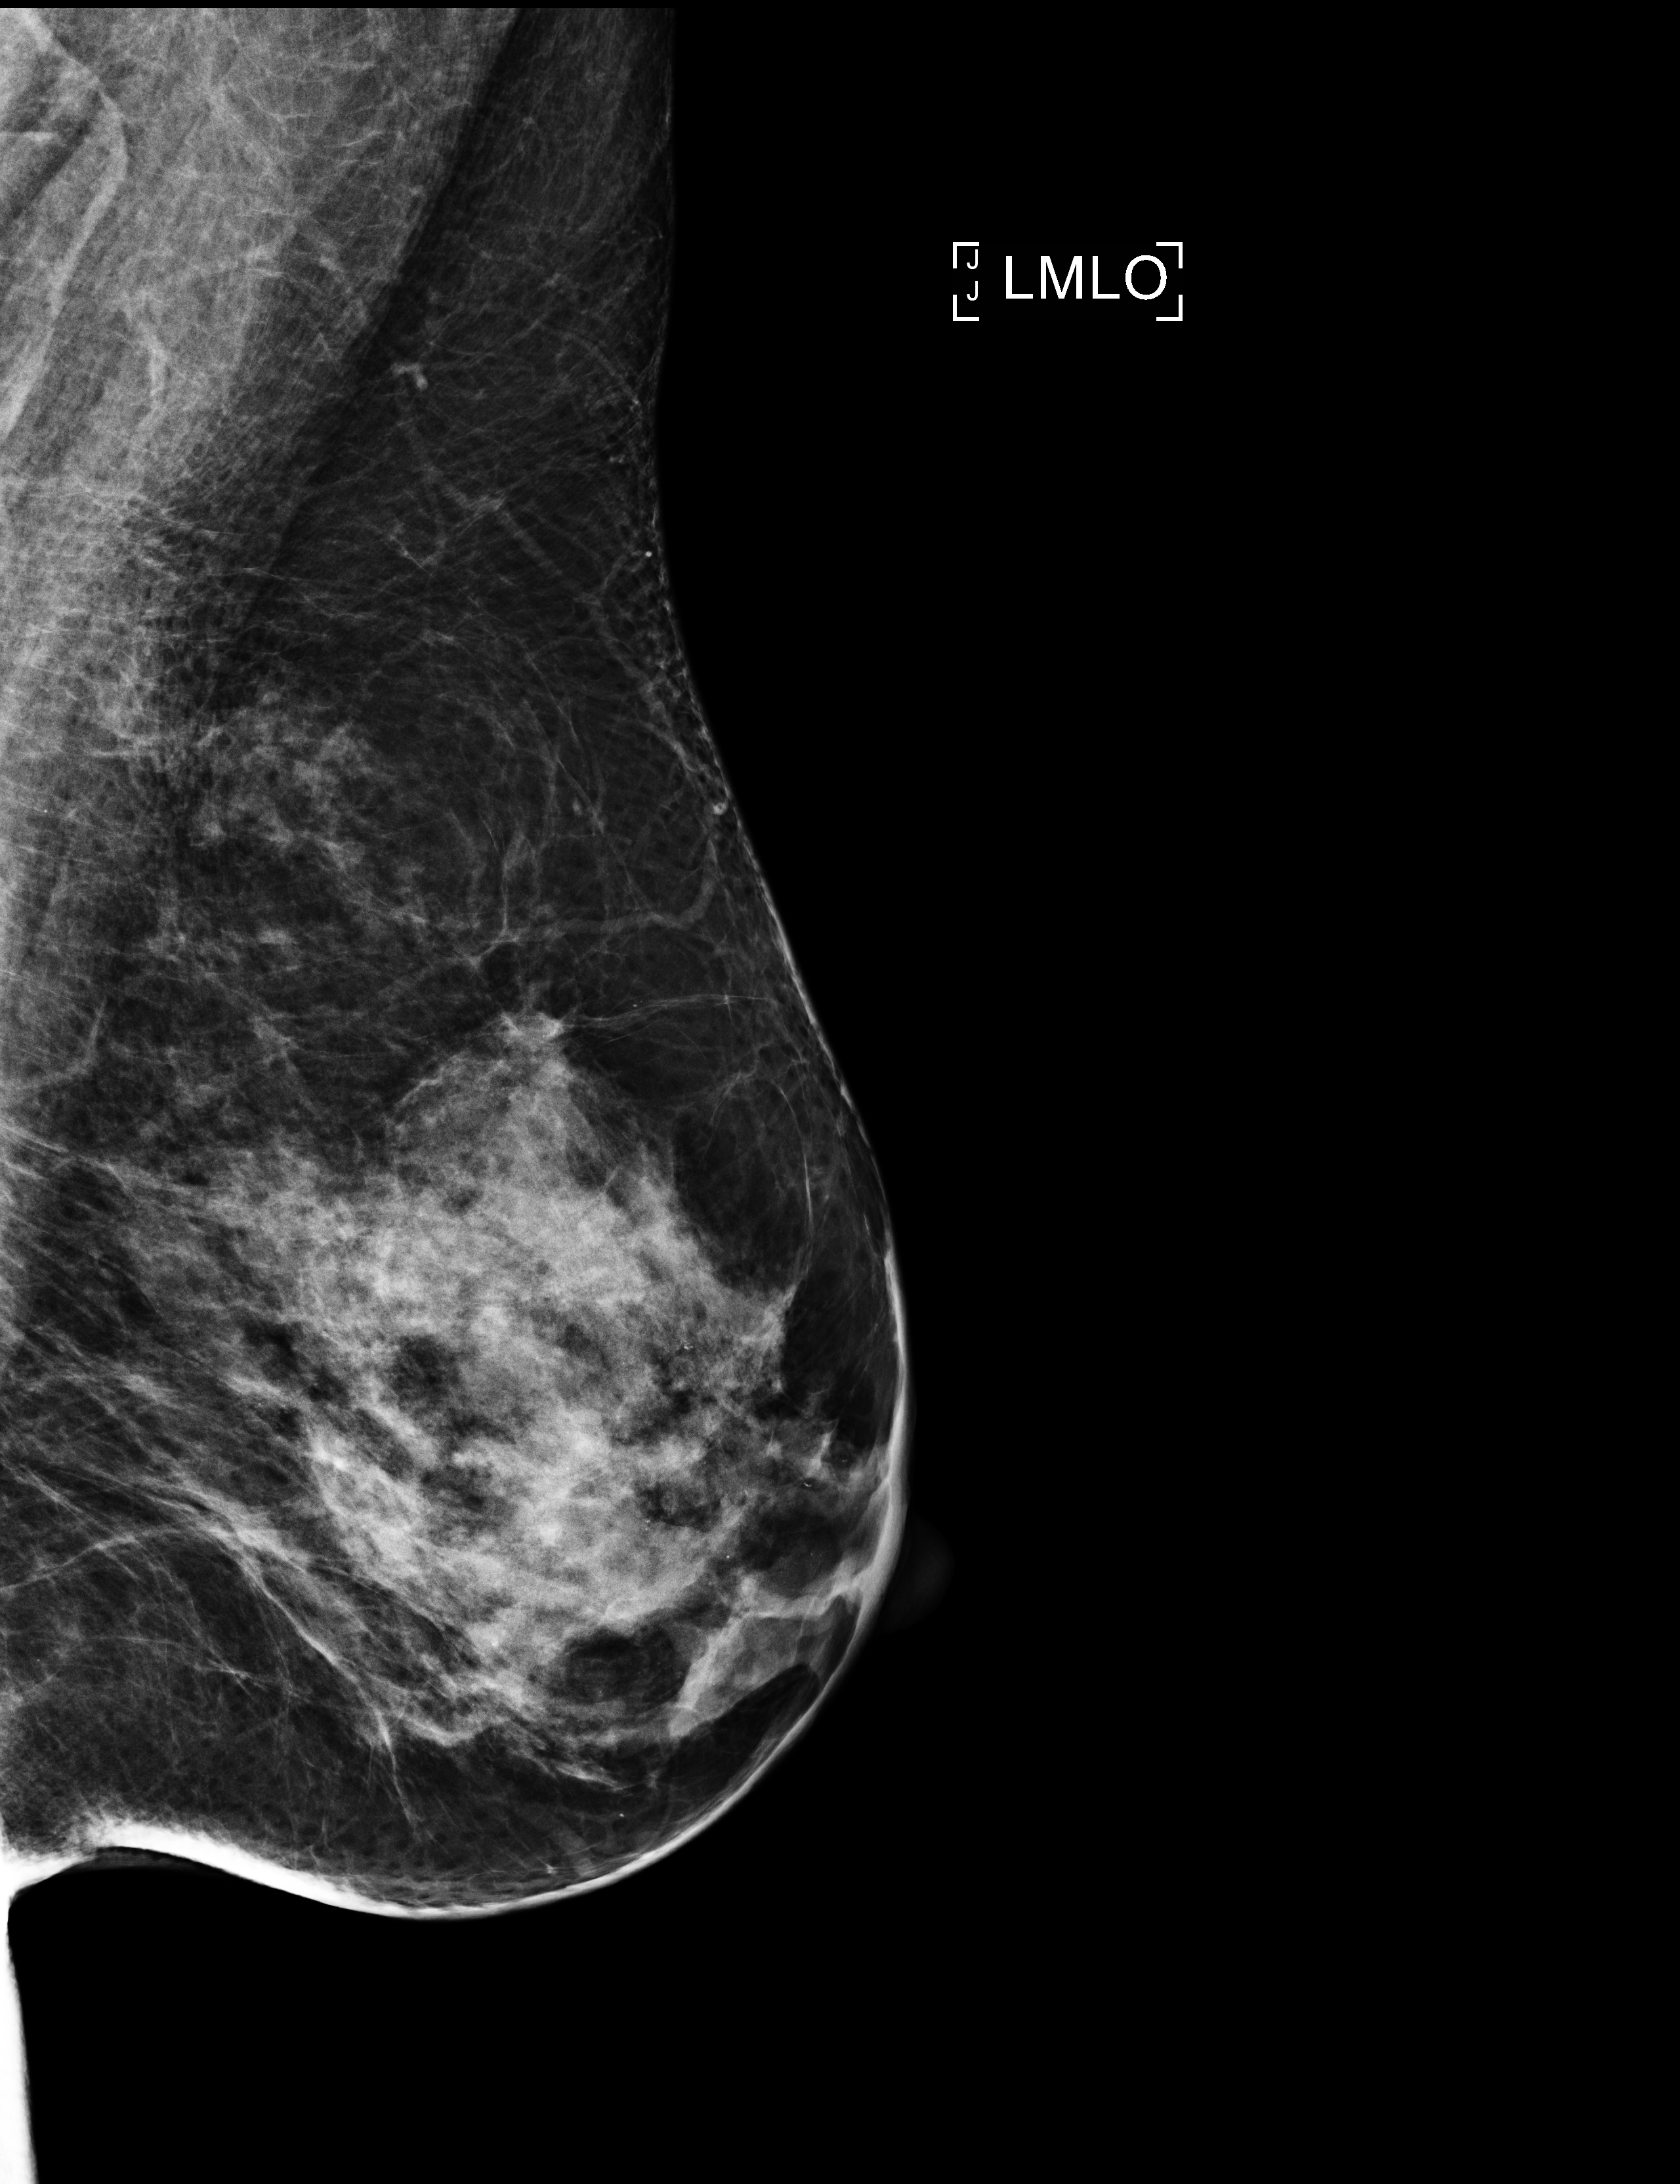
Full-field digital mammogram (FFDM); left breast; mediolateral oblique (MLO) view; screening examination. Female patient, age 55 years.
BI-RADS breast density category at the screening exam (both breasts, scale 1–4): 3. Final BI-RADS assessment for this screening round (tomosynthesis exam, both breasts): category 2. Recall: no recall after this screen.